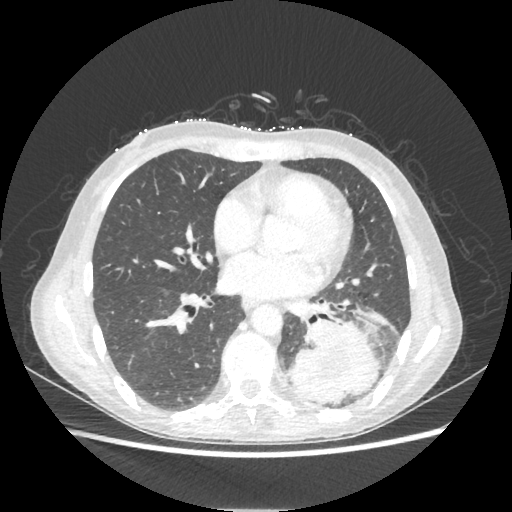
Chest CT, one axial slice; position 100 of 221 along the scan axis; reconstruction kernel STANDARD; 80 kVp; lung window (W 1500 / L -600 HU); 1.25 mm slice thickness; 512 × 512 image matrix, field of view 360 × 360 mm. Patient: female, 53 years. Case-level facts recorded for this patient, not image findings: clinical TNM (as recorded): T3 N0 M0.
Annotated regions visible in this slice (bounding box drawn by a radiologist):
- lung tumour (recorded histology: adenocarcinoma): bounding box <290,320,380,403> (left, top, right, bottom; pixels)